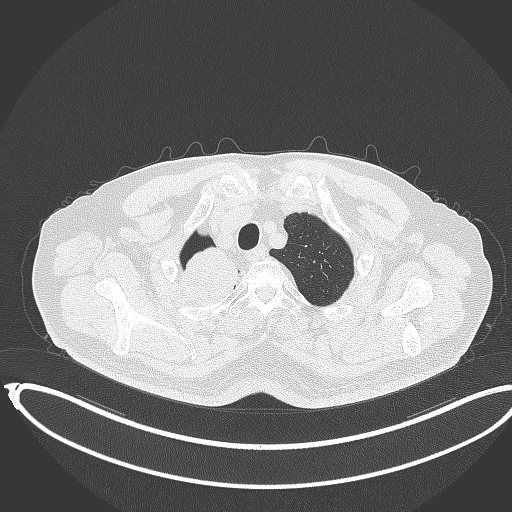
Chest CT, one axial slice. Position 329 of 403 along the scan axis. Reconstruction kernel B70f. Lung window (W 1500 / L -600 HU). 512 × 512 image matrix, field of view 436 × 436 mm. Male patient, age 68 years. Case-level facts recorded for this patient, not image findings: clinical TNM (as recorded): T2a N0 M0.
Structures marked on this image (rectangle marked by the reading radiologist):
- lung tumour (recorded histology: adenocarcinoma): bounding box <178,236,250,309> (left, top, right, bottom; pixels)